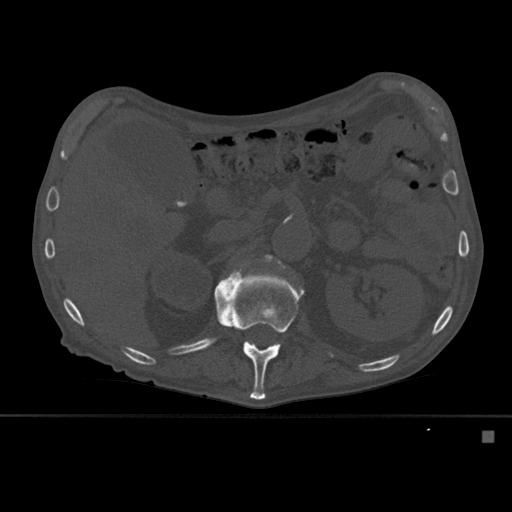
CT including the spine, one axial slice. Bone window (W 1800 / L 400 HU). 1.5 mm slice thickness. 512 × 512 image matrix, field of view 373 × 373 mm. Male patient, age 78 years. From the clinical record (not read from this slice): primary cancer: prostate.
Annotated regions visible in this slice (semi-automatically segmented with operator editing):
- L1 vertebra: bounding box <214,271,303,400> (left, top, right, bottom; pixels)
- L2 vertebra: <264,255,281,263>